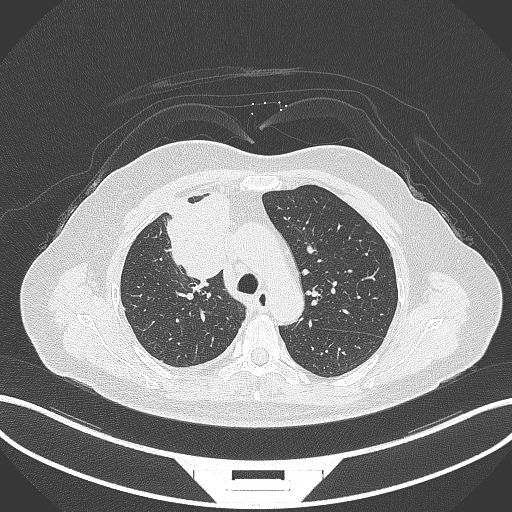
Chest CT, one axial slice; position 205 of 305 along the scan axis; reconstruction kernel B70f; lung window (W 1500 / L -600 HU); 512 × 512 image matrix, field of view 400 × 400 mm. Patient: female, 52 years. Case-level facts recorded for this patient, not image findings: clinical TNM (as recorded): T3 N1 M1.
Annotated regions visible in this slice (rectangle marked by the reading radiologist):
- lung tumour (recorded histology: adenocarcinoma): bounding box [x1, y1, x2, y2] px = [163, 189, 233, 284]